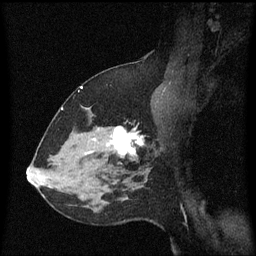
Breast MRI (dynamic contrast-enhanced), one sagittal slice; position 40 of 60 along the scan axis; dynamic contrast-enhanced series, image 2 of 3 at this slice position (ordered by acquisition); 1.5 T; TE 4.2 ms, TR 8.4 ms; 2 mm slice thickness; 256 × 256 image matrix. Female patient, age 37 years. From the clinical record (not read from this slice): setting: breast cancer imaged before/during neoadjuvant chemotherapy; receptor status: HR-positive, HER2-negative.
Outlined on this slice (semi-automatic segmentation, software-assisted and operator-edited):
- analysis volume of interest (the breast-tissue region the enhancement analysis was run in; not a lesion): bounding box (x1, y1, x2, y2) in pixels: (95, 116, 157, 171)
- tumour enhancement mask (voxels above the 70 % enhancement threshold inside the analysis volume of interest): (109, 128, 144, 157)